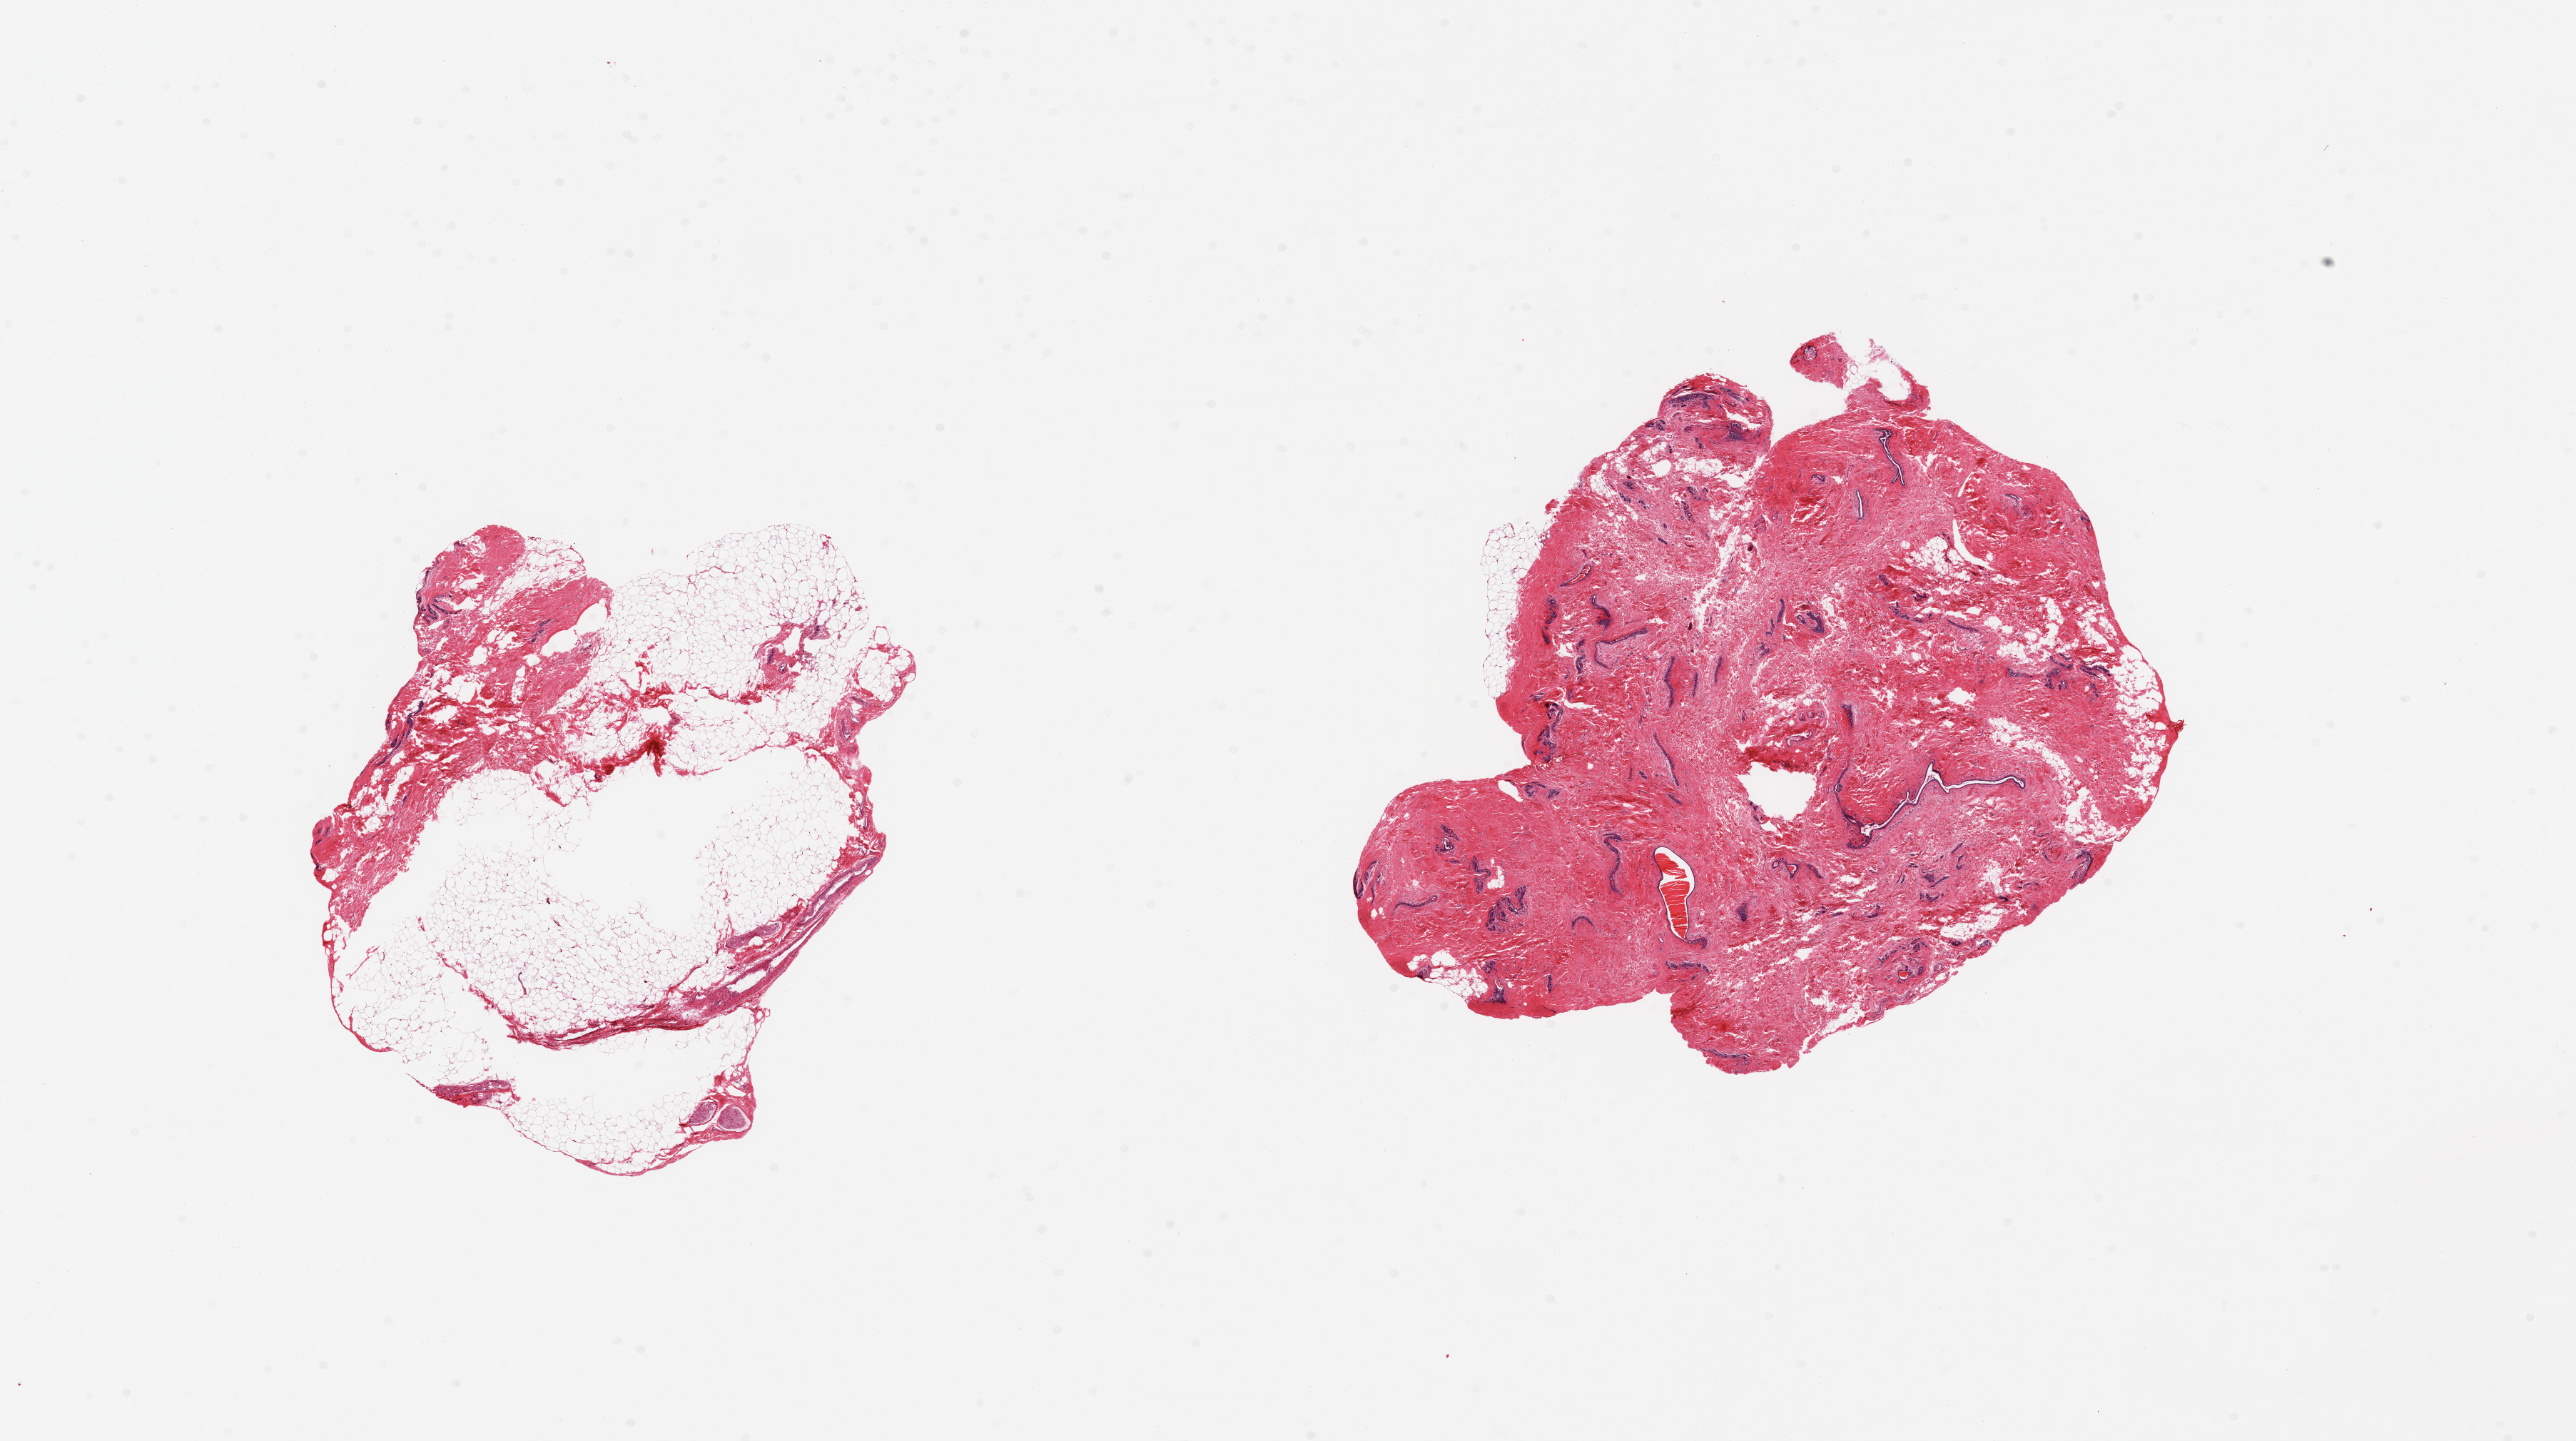
Whole-slide image, hematoxylin and eosin (H&E) stain, brightfield, shown as a low-resolution overview of the whole scanned area (about 28.5 x 16.0 mm, acquisition: 20x scan); PAXgene-fixed paraffin-embedded (PFPE) section; target tissue: breast; donor tissue sample. Donor sex: female.
Pathologist's review note for this sample: 2 pieces; 1 piece is predominantly fat (80%) with small portion of fibrous tissue/ductal elements; 2nd piece is nearly entirely dense fibrocollagenous stroma with numerous embedded ducts/lobules.